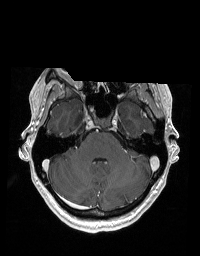
Brain MRI from a brain-tumour surgery series, one axial slice. Slice 134 of 192 in the series (ordered by position). T1-weighted post-contrast. 1 mm slice thickness. 200 × 256 image matrix, field of view 195 × 250 mm. From the clinical record (not read from this slice): histopathology: Glioblastoma; WHO grade: 2; IDH mutation: no.
Outlined on this slice (outlined manually by an expert reader):
- tumour: box from (x=75, y=108) to (x=84, y=127) px